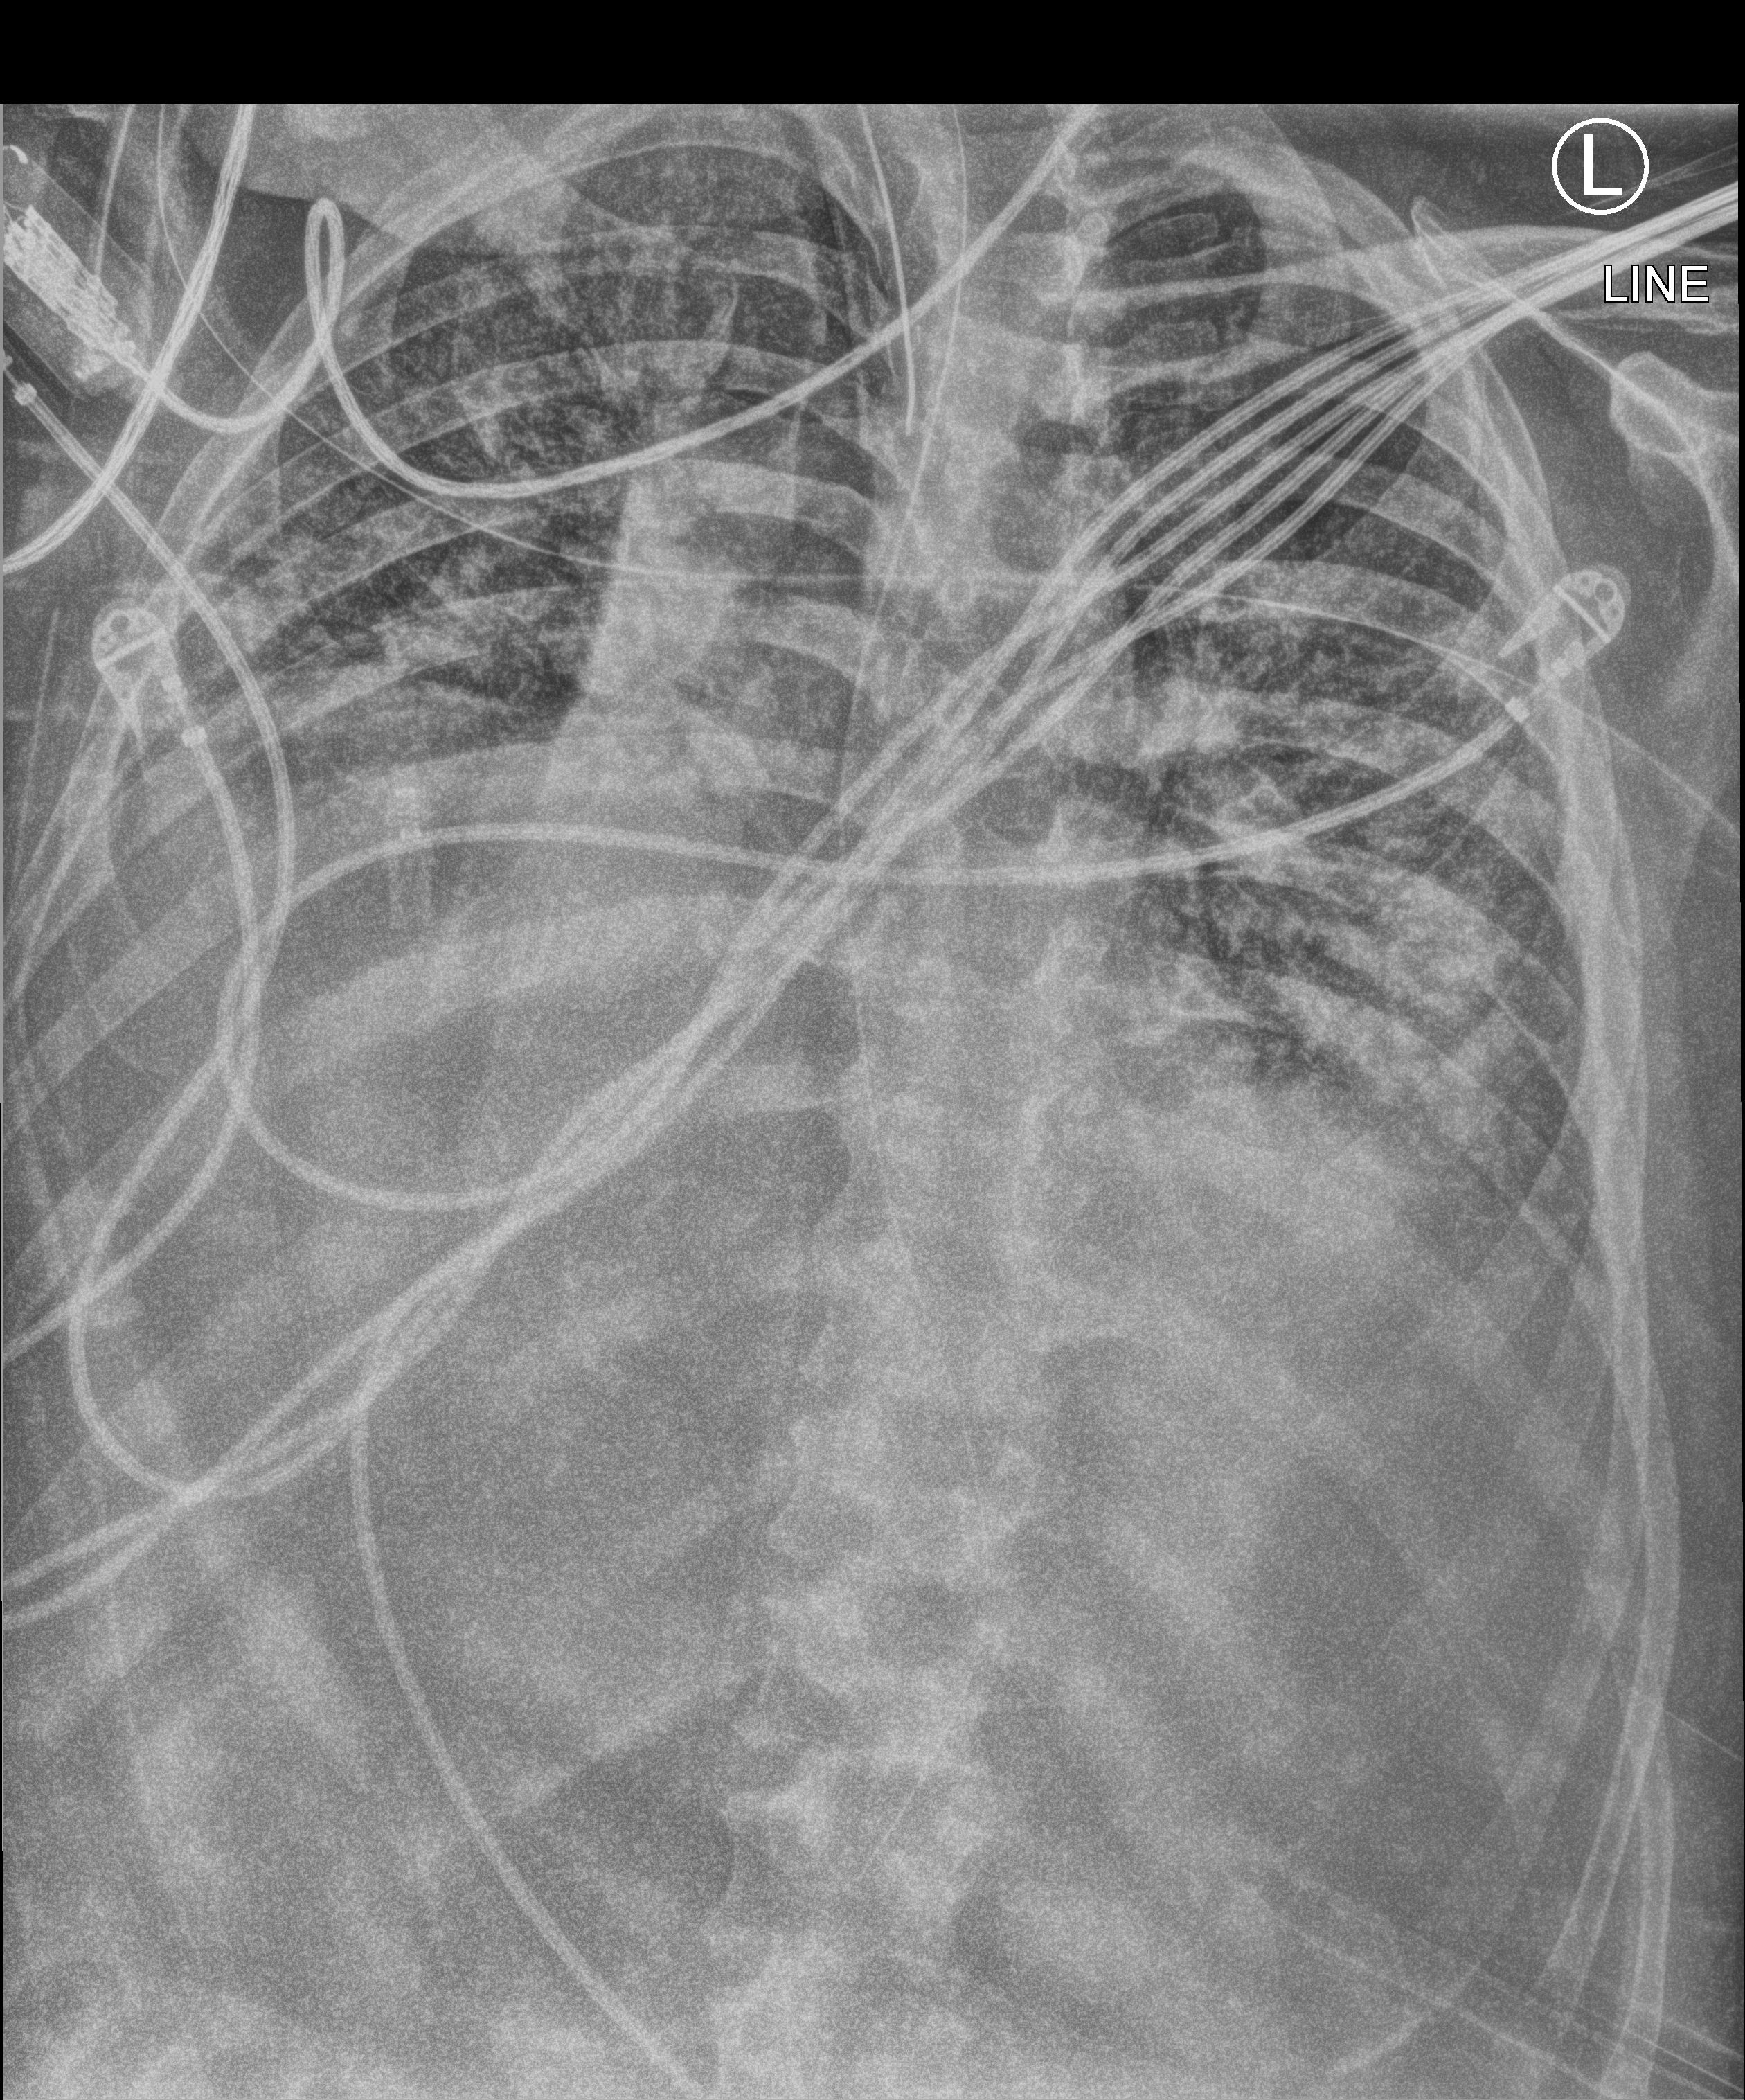
Chest X-ray (portable). Male patient hospitalised with COVID-19, age 18–59 years.
Admission-level facts for this patient (not findings on this image; timing relative to this image not recorded):
- length of hospital stay: 80 days
- smoking status (admission record): never
- mechanically ventilated during this hospital stay: yes